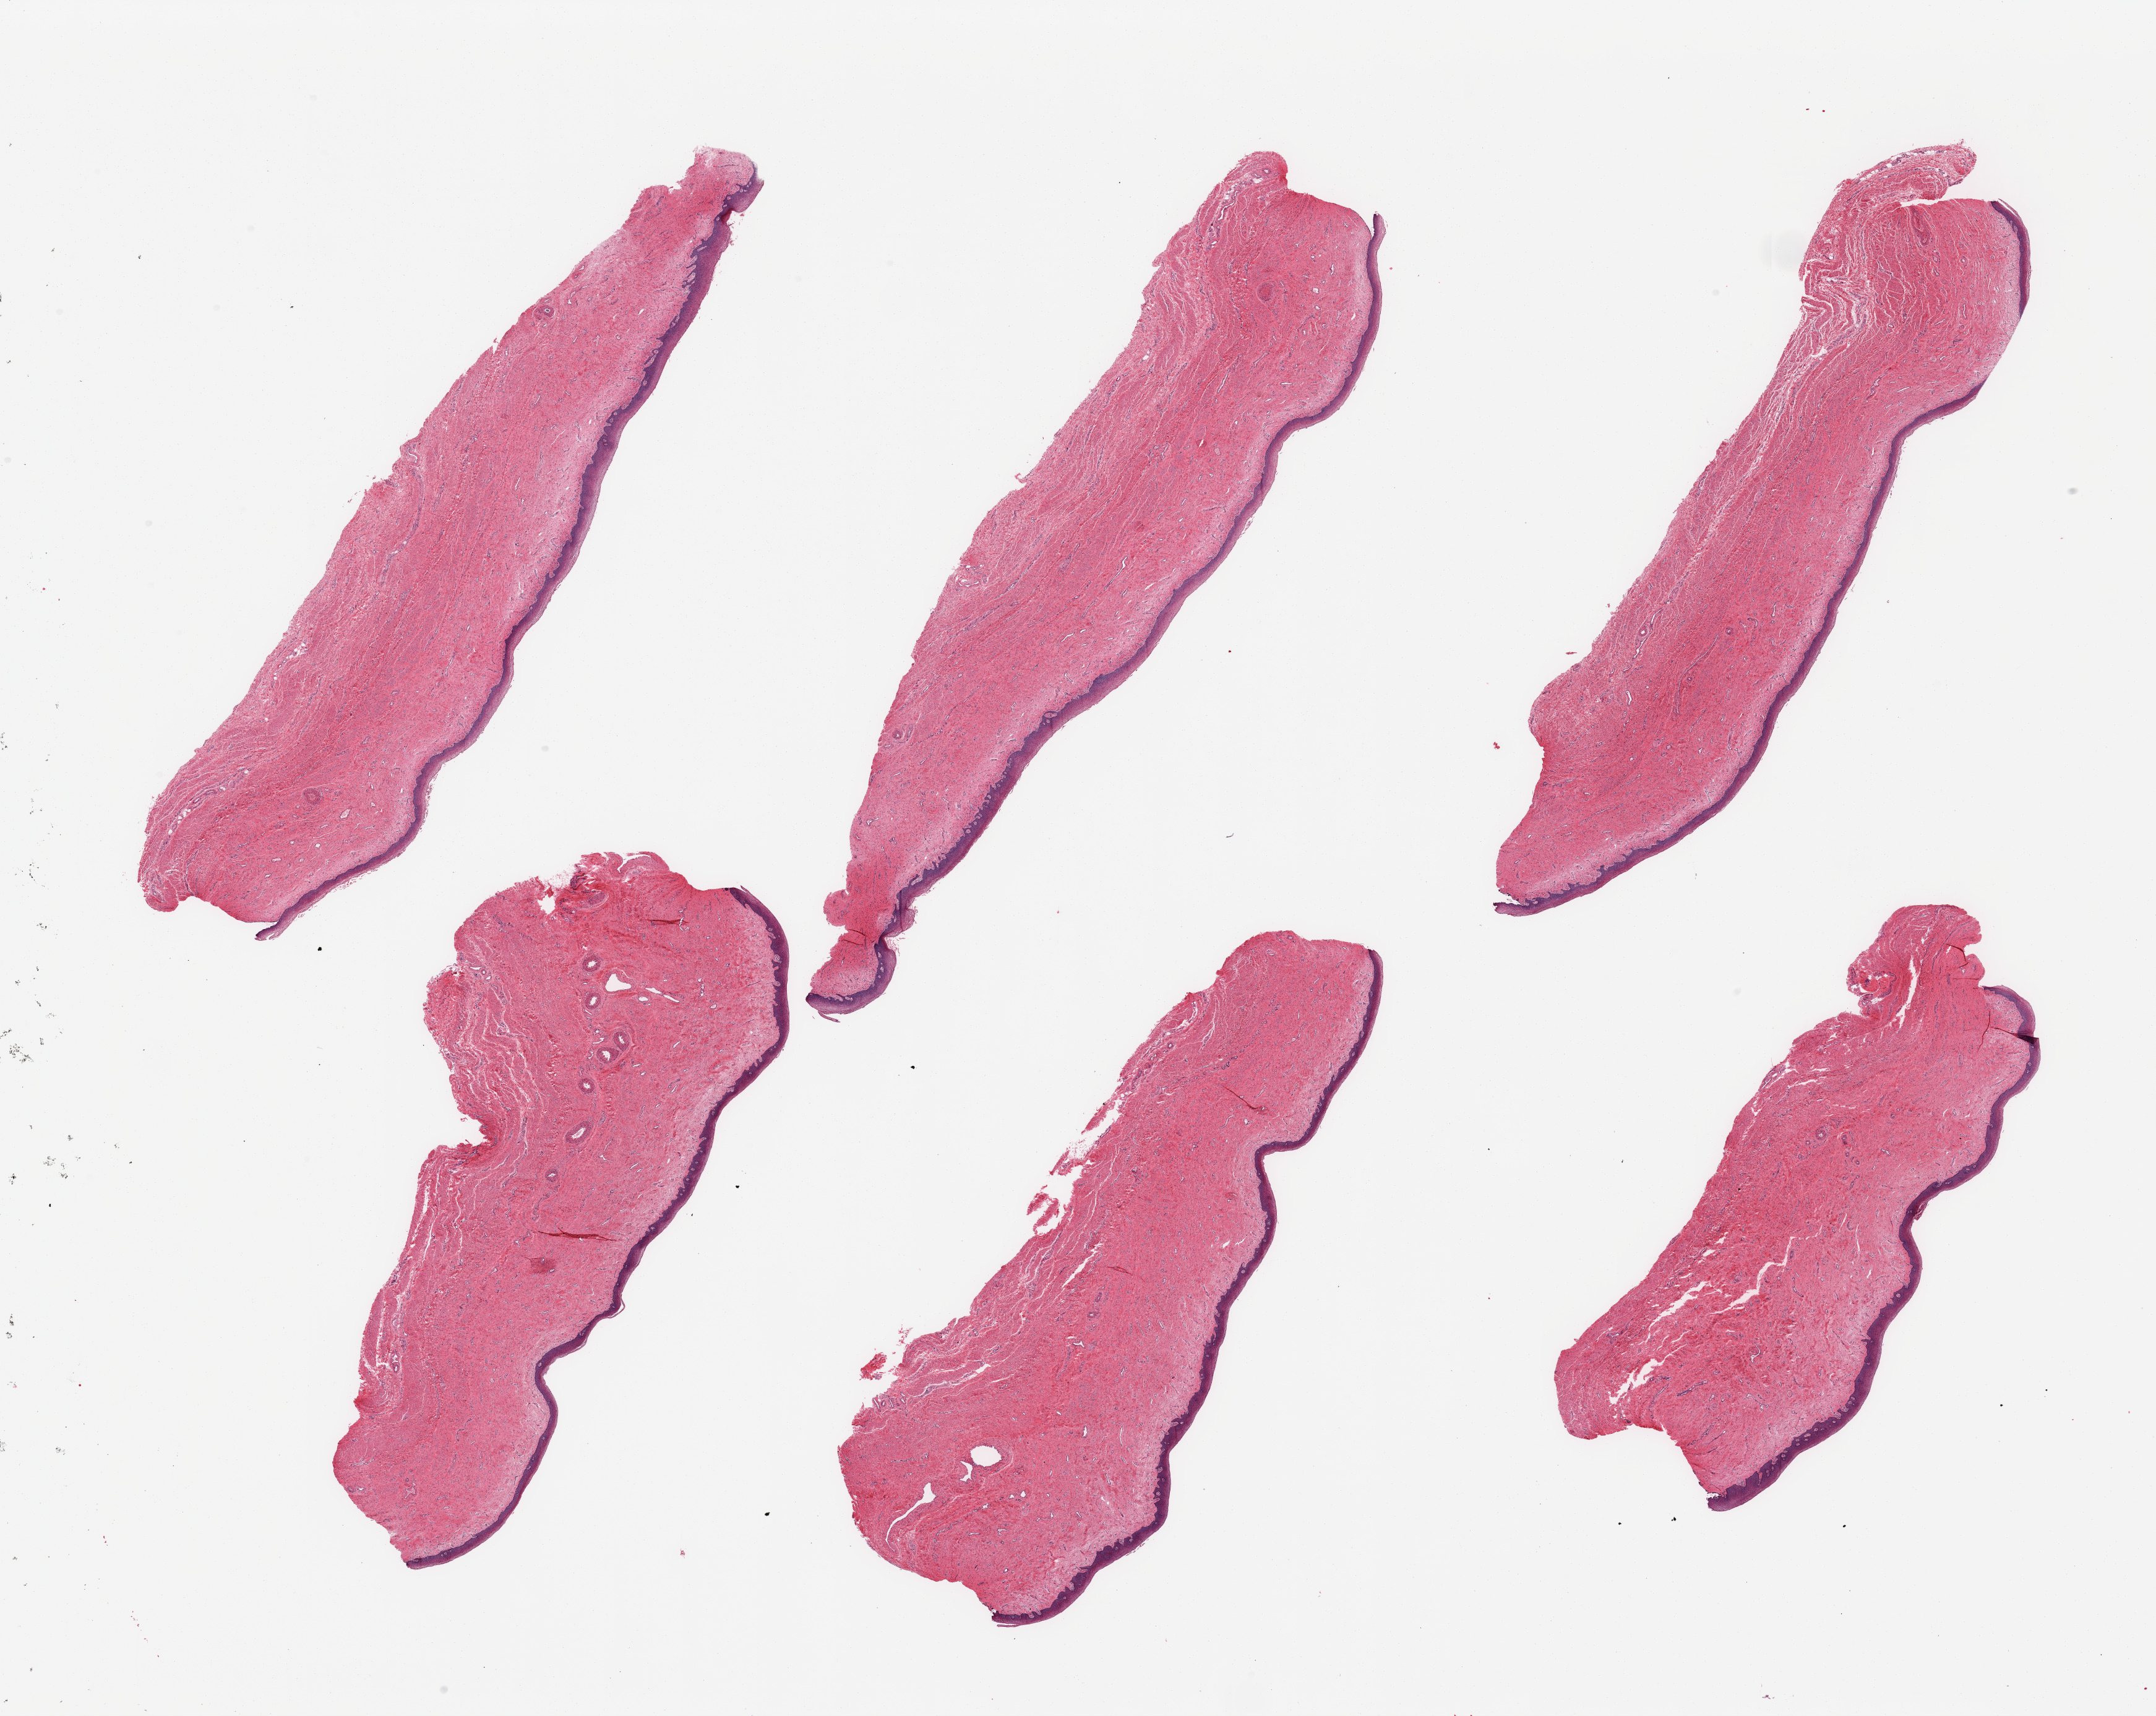
Digitized haematoxylin and eosin-stained section, brightfield — shown as a low-resolution overview of the whole scanned area (about 27.6 x 21.9 mm, slide scanned at 20x); PAXgene-fixed paraffin-embedded (PFPE) section; section of vagina (target tissue); tissue donor sample. Female donor.
Reviewer comment on this tissue sample: 6 pieces.